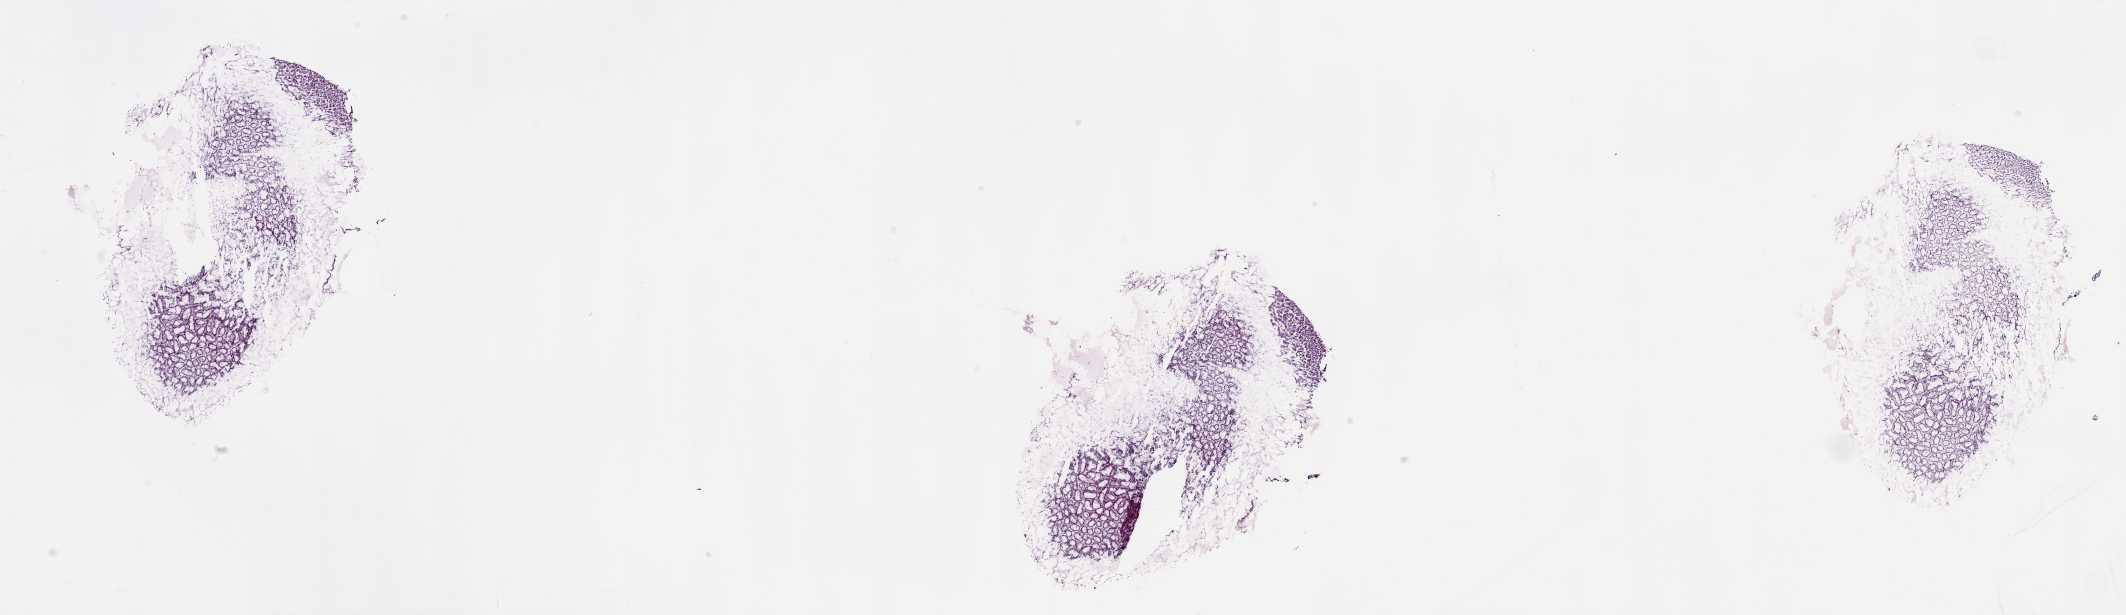
Hematoxylin and eosin (H&E) stained whole-slide image, a low-resolution overview of the entire scanned area, about 33.7 x 9.8 mm (acquisition: 20x scan); frozen section from the top of the tissue portion; solid tissue normal (non-tumour tissue) sample from the esophagus. Female, age 56 years at initial diagnosis. Slide review estimates, as recorded: tumour cells 0%, tumour nuclei 0%, normal cells 100%, stromal cells 0%, necrosis 0%. Infiltration values recorded for this section: lymphocyte infiltration 0%, monocyte infiltration 0%, neutrophil infiltration 0%.
* this section: solid tissue normal sample (biorepository sample class)
* patient diagnosis: Adenocarcinoma, NOS (lower third of esophagus)